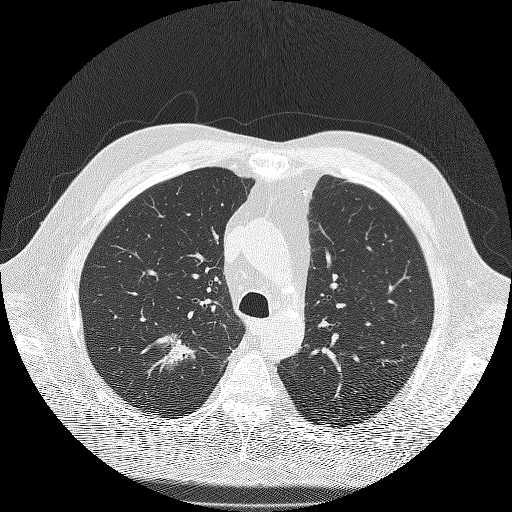
Low-dose screening chest CT, axial slice. Second screening round (one year after baseline). Lung window (W 1500 / L -600 HU). Lung (sharp) reconstruction kernel (FC51). Slice 40 of 180 in the series. Male participant, aged 71 years at enrolment. Former smoker at enrolment.
- Lesion marked by an expert reader, box from (x=136, y=325) to (x=208, y=389) px.
- The screening reader recorded 3 non-calcified nodules or masses ≥4 mm on this exam (right upper lobe, right upper lobe, right lower lobe); which of them this box marks is not recorded.
- Official screen result: positive, other.
- Later outcome: lung cancer diagnosed 59 days after this screen — bronchiolo-alveolar adenocarcinoma, NOS, right upper lobe, moderately differentiated (G2), stage IIIA (AJCC 6th edition), 25 mm at pathology.